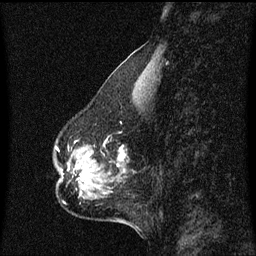
Breast MRI (dynamic contrast-enhanced), one sagittal slice; slice 22 of 60 in the series (ordered by position); dynamic contrast-enhanced series, image 2 of 3 at this slice position (ordered by acquisition); 1.5 T; TE 4.2 ms, TR 8.4 ms; 2 mm slice thickness; 256 × 256 image matrix. Female patient, age 50 years. From the clinical record (not read from this slice): setting: breast cancer imaged before/during neoadjuvant chemotherapy; receptor status: HR-positive, HER2-negative.
Structures marked on this image (semi-automatic segmentation, software-assisted and operator-edited):
- analysis volume of interest (the breast-tissue region the enhancement analysis was run in; not a lesion): bounding box (x1, y1, x2, y2) in pixels: (56, 142, 127, 191)
- tumour enhancement mask (voxels above the 70 % enhancement threshold inside the analysis volume of interest): (82, 156, 123, 181)